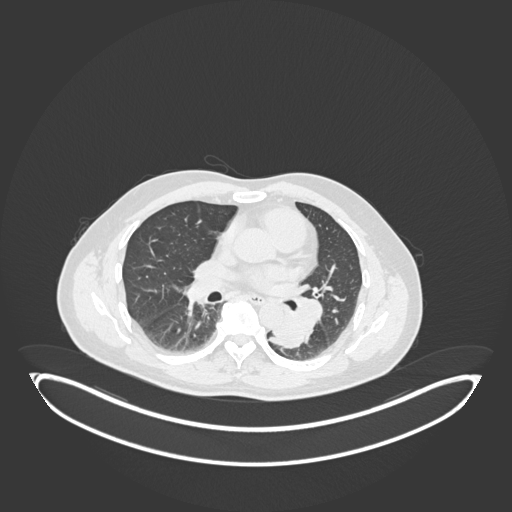
Chest CT, one axial slice; position 105 of 258 along the scan axis; reconstruction kernel B30f; 120 kVp; lung window (W 1500 / L -600 HU); 1 mm slice thickness; 512 × 512 image matrix, field of view 500 × 500 mm. Male patient, age 54 years. From the clinical record (not read from this slice): clinical TNM (as recorded): T3 N0 M0.
Structures marked on this image (bounding box drawn by a radiologist):
- lung tumour (recorded histology: squamous cell carcinoma): bounding box (x1, y1, x2, y2) in pixels: (269, 311, 306, 350)